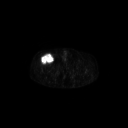
FDG PET of an extremity soft-tissue mass (from a PET/CT study), one axial slice; position 300 of 311 along the scan axis; 3.27 mm slice thickness; 128 × 128 image matrix, field of view 700 × 700 mm. Male patient, age 56 years. Case-level facts recorded for this patient, not image findings: histological type: pleiomorphic leiomyosarcoma; grade: intermediate; site of the primary tumour: right thigh.
Outlined on this slice (expert contour drawn on MRI and transferred to this co-registered scan by the dataset authors):
- gross tumour volume including surrounding oedema: bounding box (x1, y1, x2, y2) in pixels: (41, 53, 54, 64)
- gross tumour volume (mass): (41, 54, 54, 64)